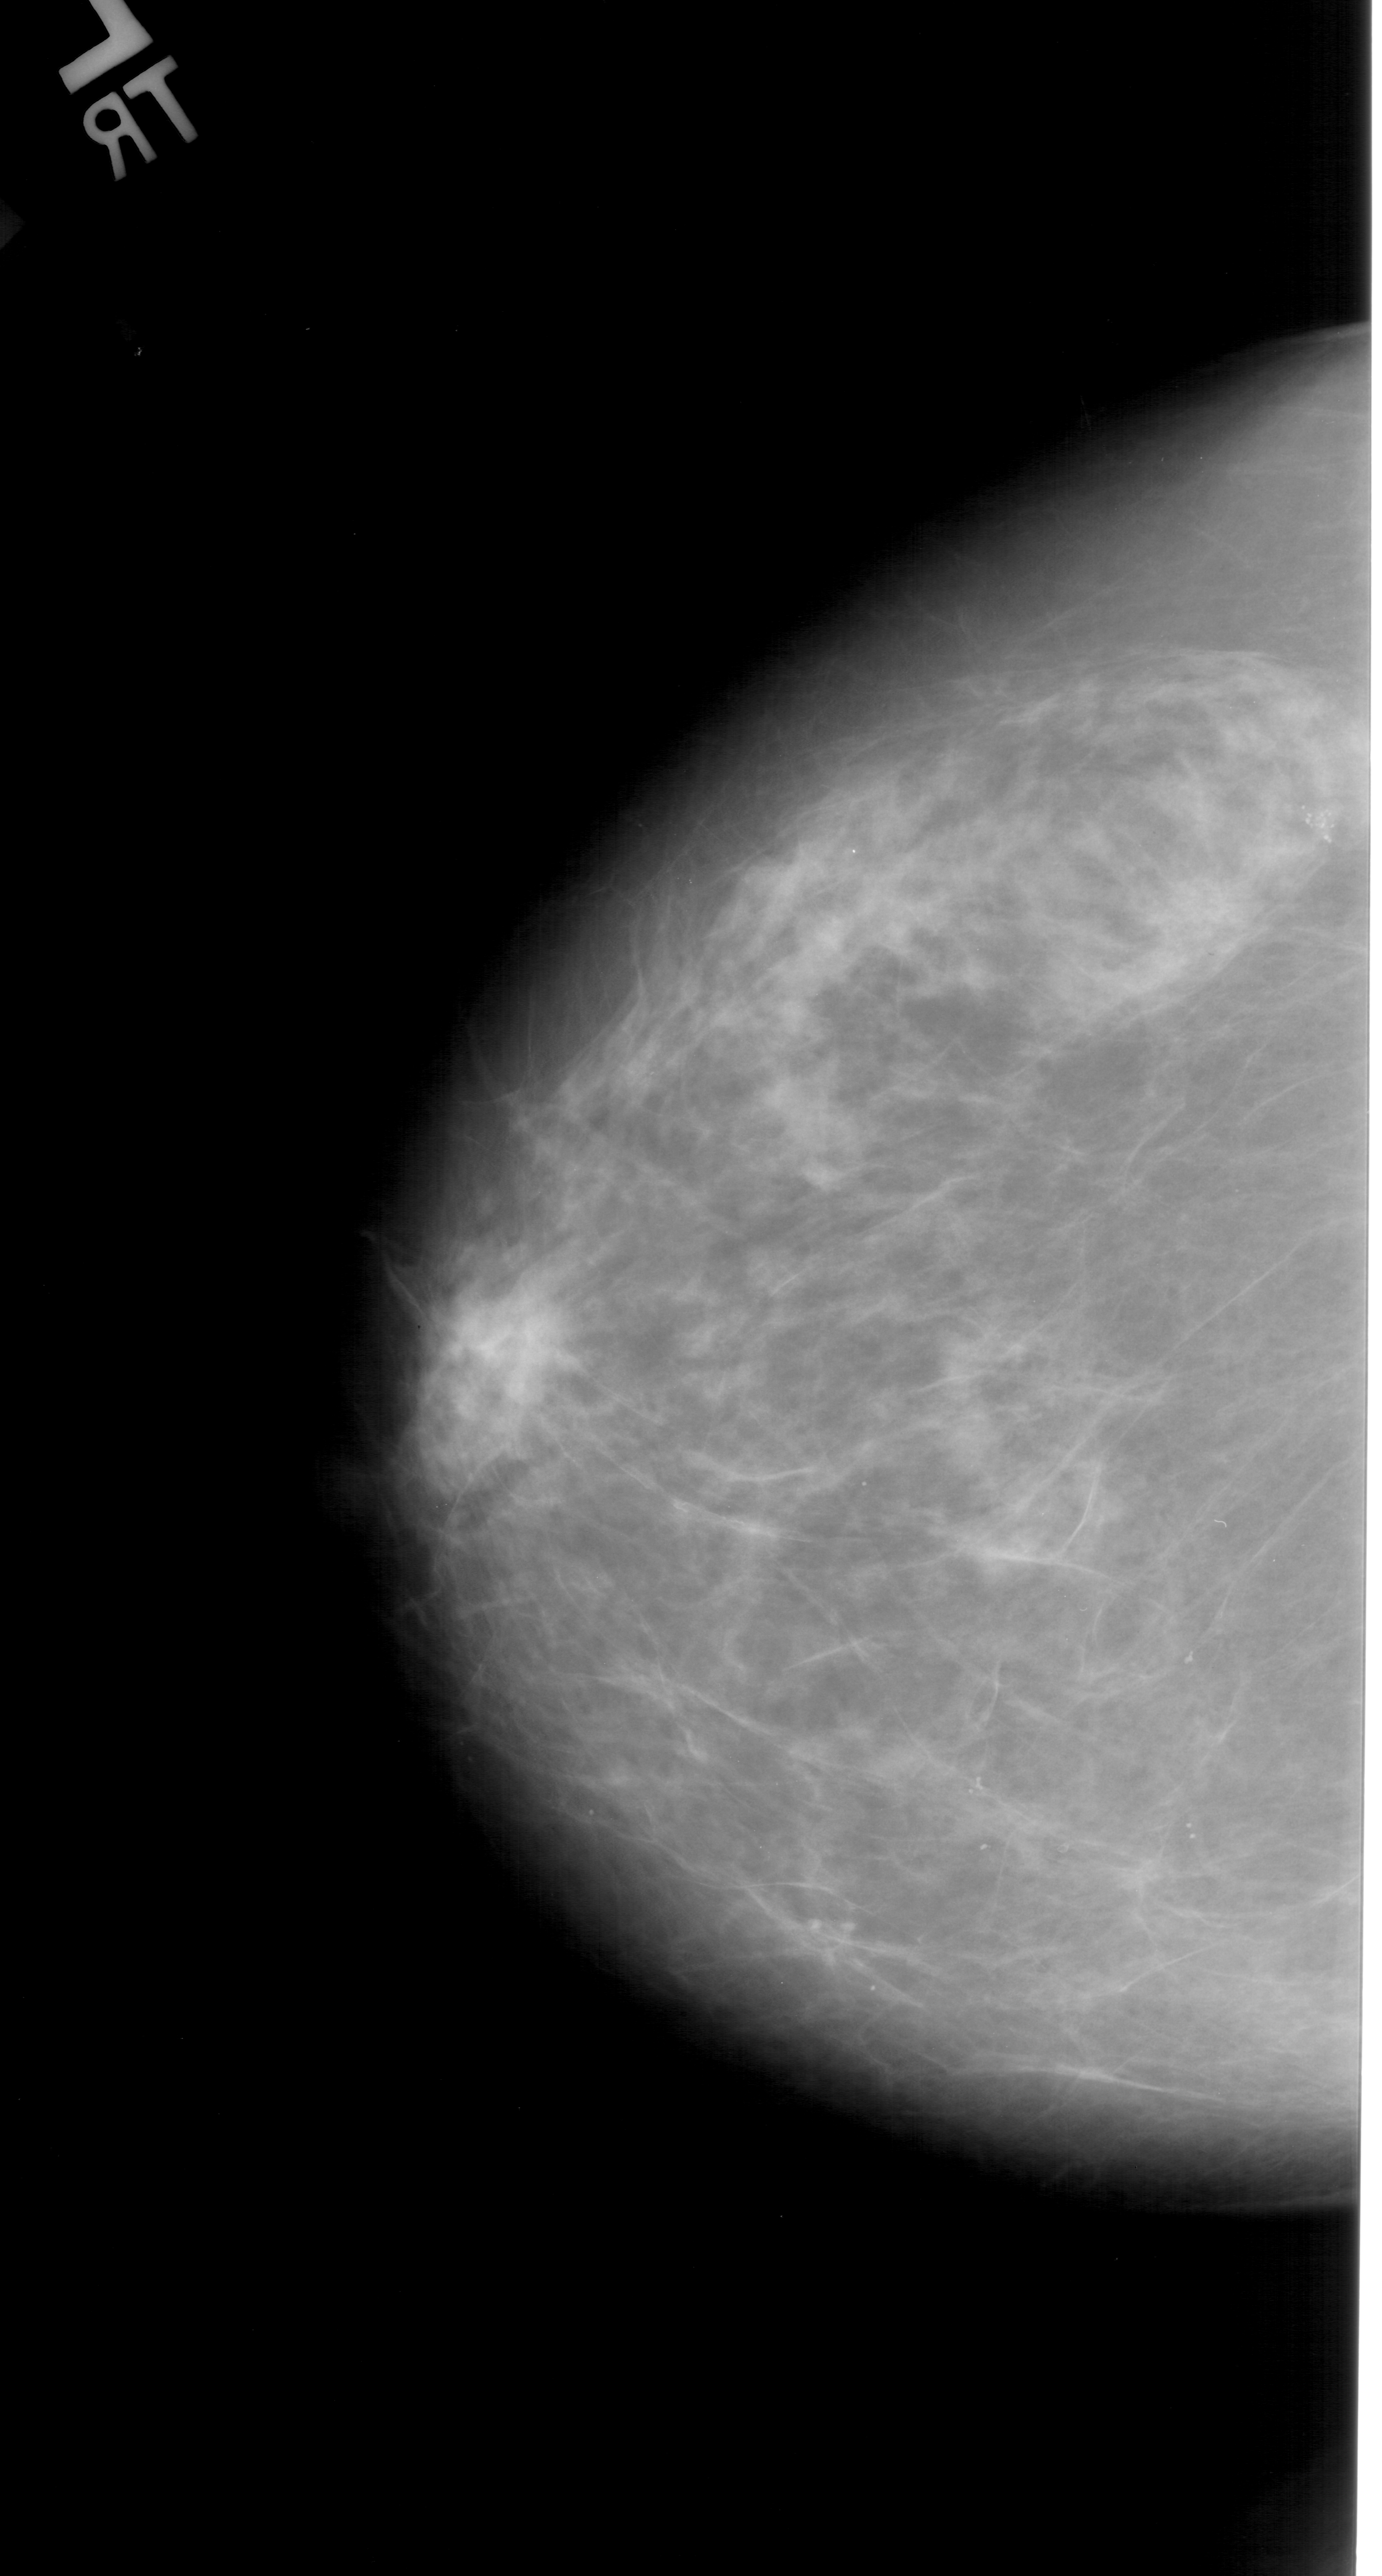
Digitized screen-film mammogram; left breast; craniocaudal (CC) view; breast composition: heterogeneously dense (BI-RADS density category 3 of 4); 1382 × 2576 image matrix.
Marked abnormalities (boxes around the expert regions of interest):
- calcifications, morphology pleomorphic, distribution clustered; BI-RADS assessment category 4; subtlety rating 4 on a 1 (subtle) to 5 (obvious) scale; pathology result (as recorded, not read from the image): malignant: bounding box (x1, y1, x2, y2) in pixels: (1292, 792, 1360, 854)